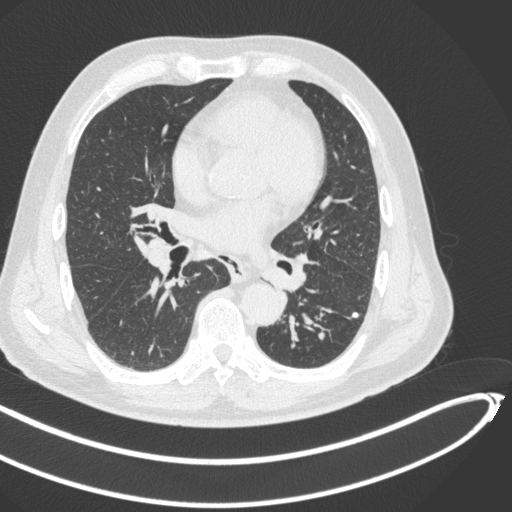
Chest CT, one axial slice. Slice 234 of 466 in the series (ordered by position). Reconstruction kernel B31f. Lung window (W 1500 / L -600 HU). 512 × 512 image matrix, field of view 400 × 400 mm. Patient: male, 64 years. Case-level facts recorded for this patient, not image findings: clinical TNM (as recorded): T1c N0 M0; histopathological grade: G2.
Outlined on this slice (rectangle marked by the reading radiologist):
- lung tumour (recorded histology: squamous cell carcinoma): bounding box [x1, y1, x2, y2] px = [254, 261, 295, 295]